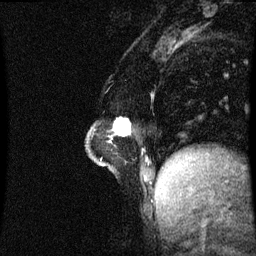
Breast MRI (dynamic contrast-enhanced), one sagittal slice. Position 17 of 60 along the scan axis. Dynamic contrast-enhanced series, image 2 of 3 at this slice position (ordered by acquisition). 1.5 T. TE 4.2 ms, TR 8.9 ms. 256 × 256 image matrix, field of view 200 × 200 mm. Female patient, age 47 years. Case-level facts recorded for this patient, not image findings: setting: breast cancer imaged before/during neoadjuvant chemotherapy; receptor status: HR-positive, HER2-negative.
Structures marked on this image (semi-automatically segmented with operator editing):
- analysis volume of interest (the breast-tissue region the enhancement analysis was run in; not a lesion): box from (x=88, y=122) to (x=132, y=163) px
- tumour enhancement mask (voxels above the 70 % enhancement threshold inside the analysis volume of interest): (x=115, y=122)–(x=130, y=135)